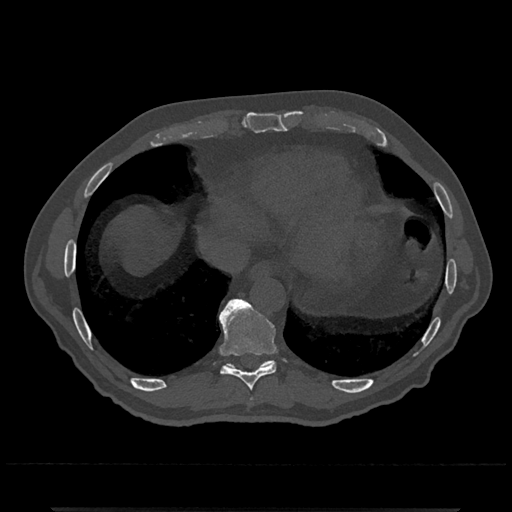
CT including the spine, one axial slice. Position 600 of 797 along the scan axis. Reconstruction kernel Br40s/3. 120 kVp. Bone window (W 1800 / L 400 HU). 0.5 mm slice thickness. 512 × 512 image matrix, field of view 393 × 393 mm. Male patient, age 67 years. Case-level facts recorded for this patient, not image findings: primary cancer: prostate.
Annotated regions visible in this slice (semi-automatically segmented with operator editing):
- T10 vertebra: bounding box (x1, y1, x2, y2) in pixels: (226, 299, 275, 367)
- T9 vertebra: (219, 298, 276, 391)